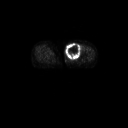
FDG PET of an extremity soft-tissue mass (from a PET/CT study), one axial slice; 3.27 mm slice thickness; 128 × 128 image matrix, field of view 700 × 700 mm. Patient: female, 74 years. Case-level facts recorded for this patient, not image findings: histological type: pleomorphic leiomyosarcoma; grade: high; site of the primary tumour: left thigh.
Structures marked on this image (expert contour drawn on MRI and transferred to this co-registered scan by the dataset authors):
- gross tumour volume including surrounding oedema: bounding box [x1, y1, x2, y2] px = [65, 42, 82, 60]
- gross tumour volume (mass): [65, 42, 81, 60]